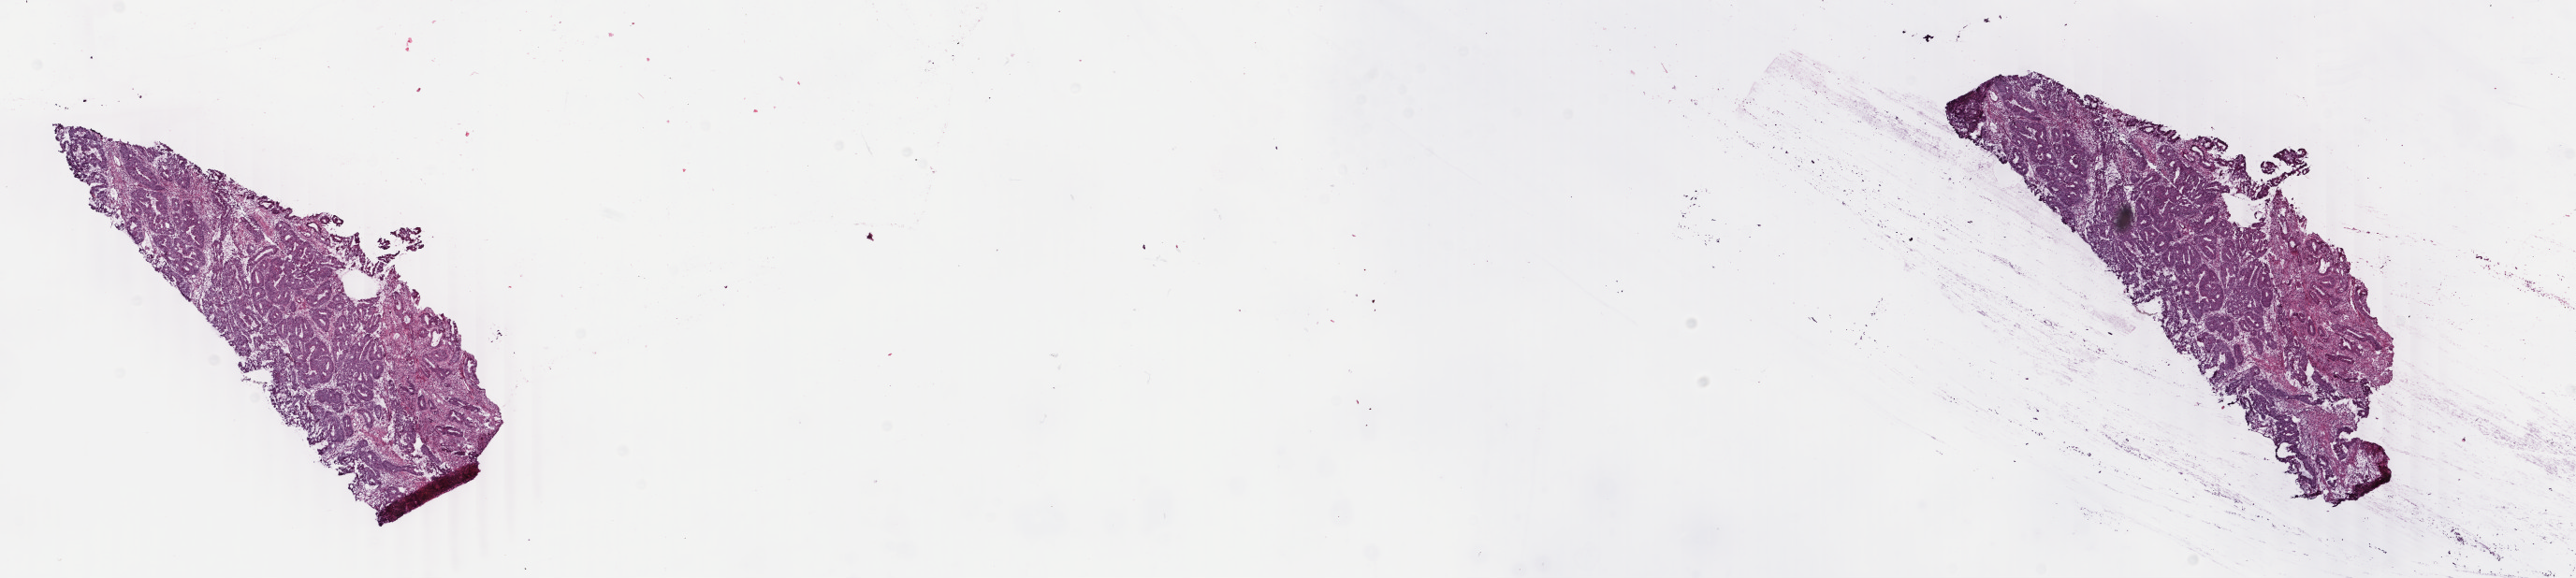
Whole-slide histology image, H&E, low-resolution overview of the scanned area, about 21.9 x 4.9 mm (acquisition: 40x scan); frozen section; primary tumour sample from the rectum. Patient: male, age at initial diagnosis 55 years. Composition of this section per pathologist review: tumour cells 95%, tumour nuclei 85%, normal cells 0%, stromal cells 4%, necrosis 1%. Infiltration values recorded for this section: lymphocyte infiltration 8%, monocyte infiltration 4%, neutrophil infiltration 0%.
- diagnosis: Adenocarcinoma, NOS
- AJCC pathologic stage: IV (6th edition)
- lymph nodes positive (case pathology): 4 of 19 examined